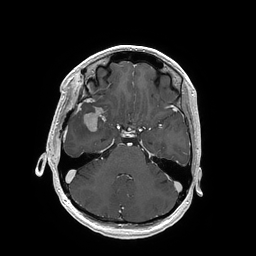
Brain MRI from a brain-tumour surgery series, one axial slice. Slice 116 of 202 in the series (ordered by position). T1-weighted post-contrast. 256 × 256 image matrix, field of view 250 × 250 mm. From the clinical record (not read from this slice): histopathology: Glioblastoma; WHO grade: 4; IDH mutation: no; tumour location: Right Insular.
Outlined on this slice (outlined manually by an expert reader):
- tumour: bounding box [x1, y1, x2, y2] px = [83, 107, 102, 131]